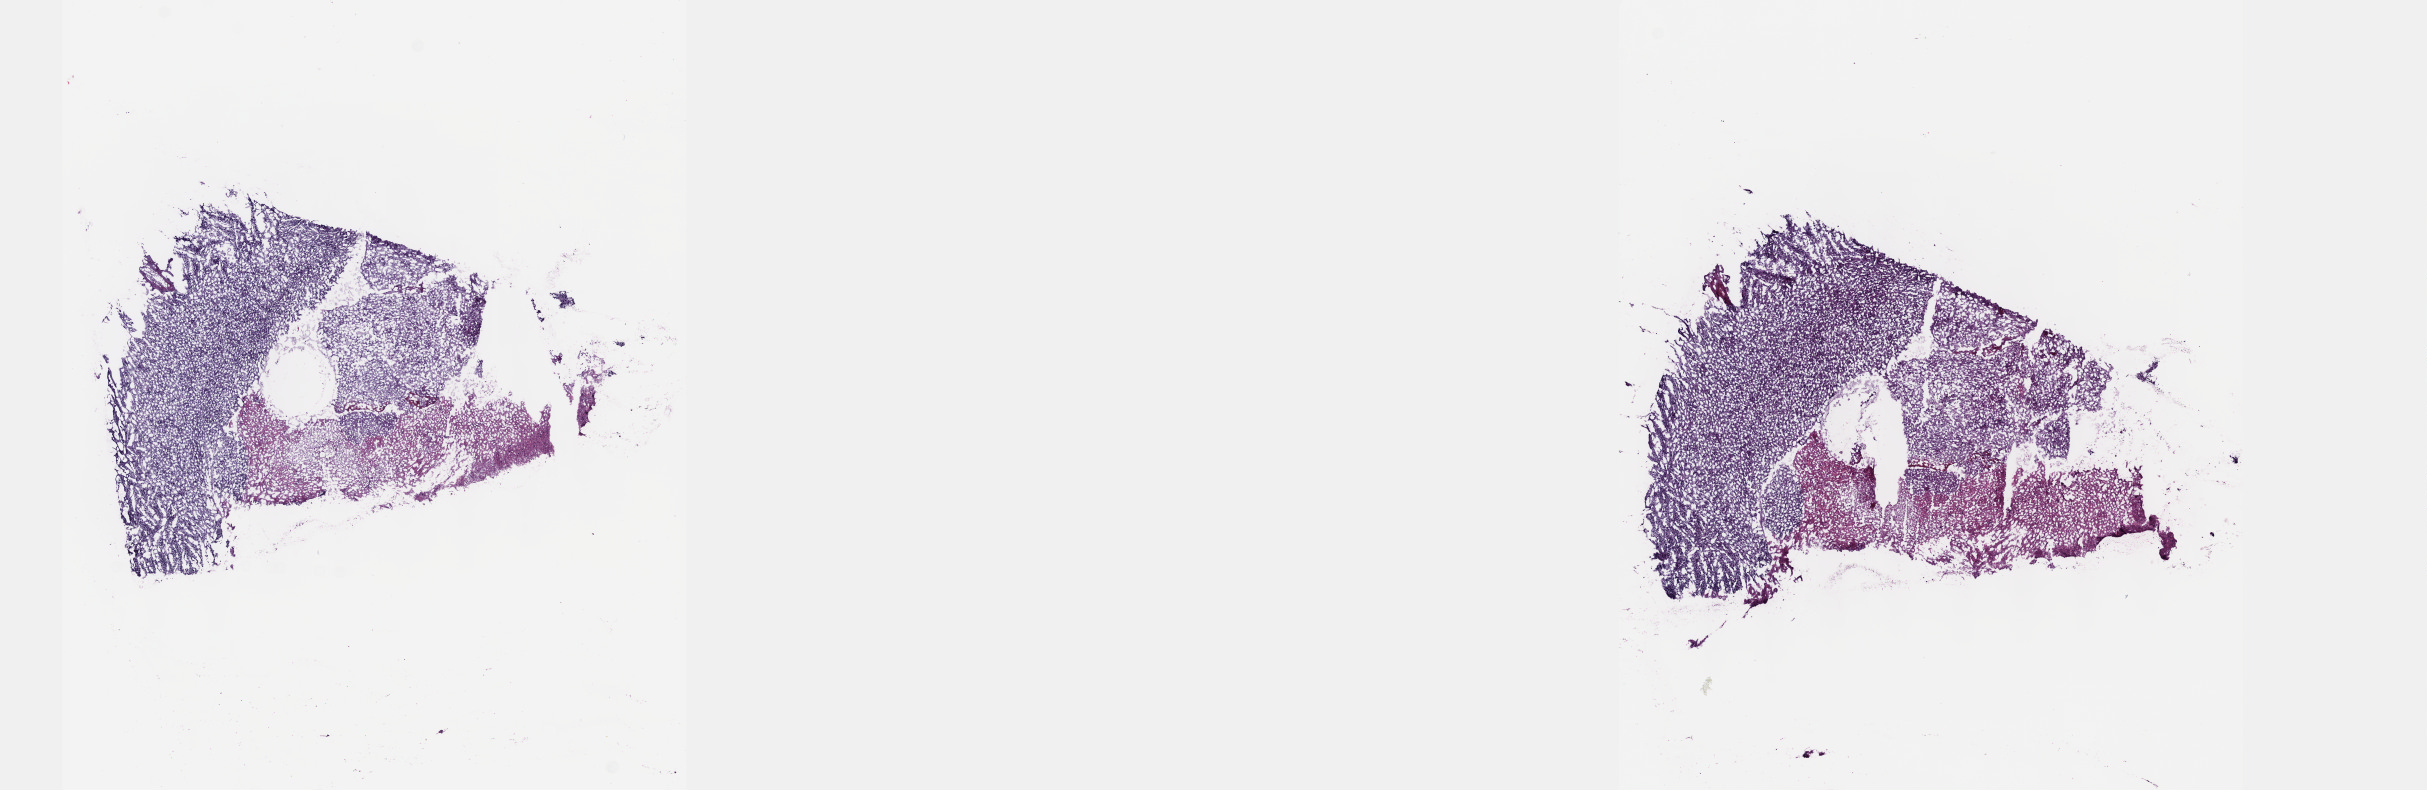
Whole-slide histology image, Hematoxylin and eosin (H&E) stained — a low-resolution overview of the entire scanned area, about 19.6 x 6.4 mm (from a 40x scan). Frozen section from the top of the tissue portion. Primary tumour sample from the brain. Male, age 47 years at initial diagnosis. Slide review estimates, as recorded: tumour cells 70%, tumour nuclei 90%, normal cells 5%, stromal cells 25%, necrosis 0%. Infiltration values recorded for this section: lymphocyte infiltration 0%, monocyte infiltration 0%, neutrophil infiltration 0%.
Diagnosis: Glioblastoma.